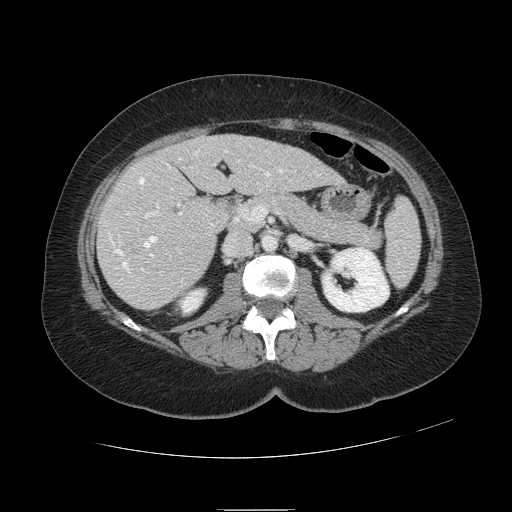
Contrast-enhanced abdominal CT, one axial slice; position 46 of 121 along the scan axis; 120 kVp; intravenous contrast given; soft-tissue window (W 400 / L 40 HU); 2.5 mm slice thickness; 512 × 512 image matrix. Female patient, age 52 years. From the clinical record (not read from this slice): diagnosis: colorectal cancer liver metastases, imaged before liver resection; multiple liver metastases: yes; largest metastasis: 6.3 cm; disease in both lobes: no.
Structures marked on this image (outlined manually by an expert reader):
- hepatic veins: bounding box <110,151,282,272> (left, top, right, bottom; pixels)
- liver: <99,135,341,310>
- planned liver remnant (the part of the liver to remain after resection): <175,135,341,195>
- portal vein (with intrahepatic branches): <126,161,240,270>